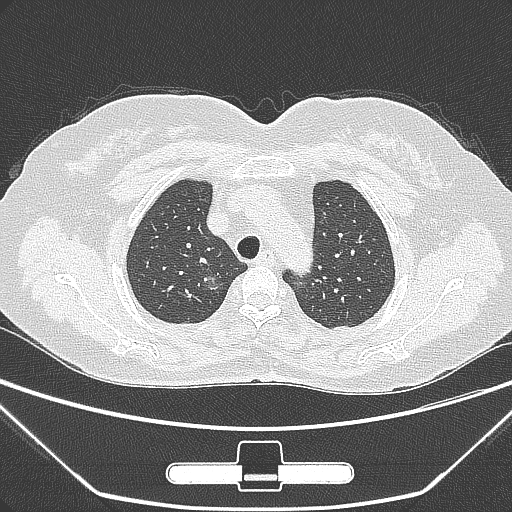
Chest CT, one axial slice; 120 kVp; lung window (W 1500 / L -600 HU); 1 mm slice thickness; 512 × 512 image matrix, field of view 356 × 356 mm. Patient: female, 63 years. From the clinical record (not read from this slice): clinical TNM (as recorded): T1a N0 M0; histopathological grade: G1.
Annotated regions visible in this slice (rectangle marked by the reading radiologist):
- lung tumour (recorded histology: adenocarcinoma): box from (x=193, y=262) to (x=222, y=297) px